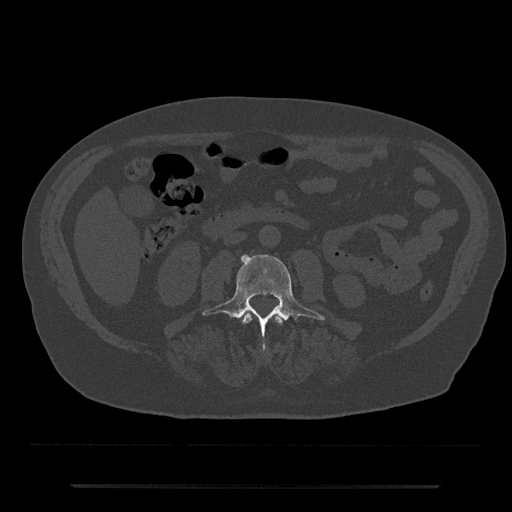
CT including the spine, one axial slice. Position 418 of 797 along the scan axis. Reconstruction kernel Br40s/3. 120 kVp. Bone window (W 1800 / L 400 HU). 0.5 mm slice thickness. 512 × 512 image matrix. Male patient, age 80 years. Case-level facts recorded for this patient, not image findings: primary cancer: prostate.
Structures marked on this image (semi-automatic segmentation, software-assisted and operator-edited):
- L2 vertebra: bounding box <243,314,282,324> (left, top, right, bottom; pixels)
- L3 vertebra: <202,254,324,350>